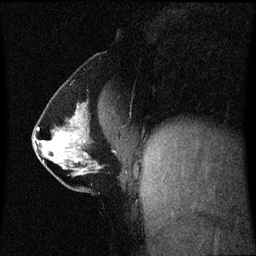
Breast MRI (dynamic contrast-enhanced), one sagittal slice; position 28 of 60 along the scan axis; dynamic contrast-enhanced series, image 2 of 3 at this slice position (ordered by acquisition); 1.5 T; TE 4.2 ms, TR 8.4 ms; 2 mm slice thickness; 256 × 256 image matrix, field of view 210 × 210 mm. Patient: female, 40 years. Case-level facts recorded for this patient, not image findings: setting: breast cancer imaged before/during neoadjuvant chemotherapy; receptor status: triple-negative.
Structures marked on this image (semi-automatic segmentation, software-assisted and operator-edited):
- analysis volume of interest (the breast-tissue region the enhancement analysis was run in; not a lesion): bounding box [x1, y1, x2, y2] px = [33, 112, 113, 188]
- tumour enhancement mask (voxels above the 70 % enhancement threshold inside the analysis volume of interest): [38, 128, 78, 162]